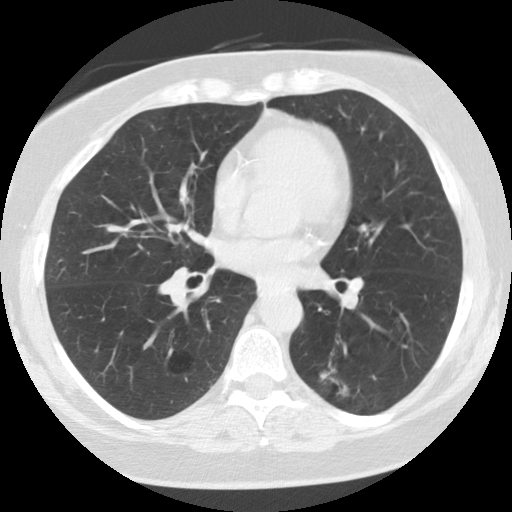
Low-dose screening chest CT, axial slice. First (baseline) screen. Lung window (W 1500 / L -600 HU). Standard (soft-tissue) reconstruction kernel (STANDARD). 120 kVp. 512 × 512 image matrix, field of view 315 × 315 mm. Female participant, aged 59 years at enrolment. Current smoker at enrolment.
- Expert reader's lesion annotation, bounding box (x1, y1, x2, y2) in pixels: (294, 351, 365, 417).
- The screening reader recorded 5 non-calcified nodules or masses ≥4 mm on this exam (right upper lobe, right lower lobe, left lower lobe, right lower lobe, left lower lobe); which of them this box marks is not recorded.
- Official screen result: positive, change unspecified: nodule(s) >= 4 mm or enlarging nodule(s), mass(es), or other non-specific abnormalities suspicious for lung cancer.
- Participant outcome: lung cancer diagnosed 707 days after this screen — adenocarcinoma, NOS, left lower lobe, poorly differentiated (G3), stage IA (AJCC 6th edition), 15 mm at pathology.